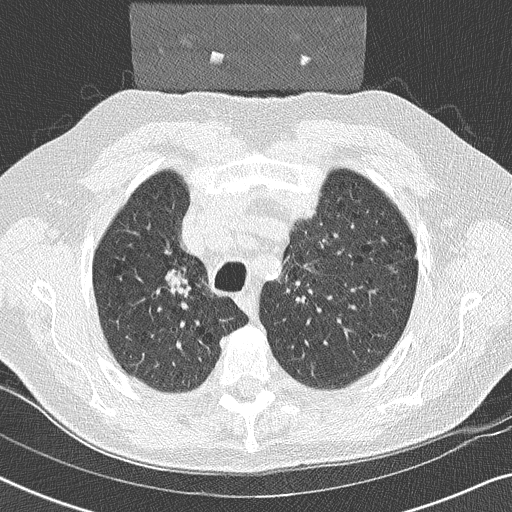
Low-dose screening chest CT, one axial slice; slice 185 of 252 in the series (ordered by position); 120 kVp; lung window (W 1500 / L -600 HU); 2 mm slice thickness; 512 × 512 image matrix, field of view 330 × 330 mm.
Structures marked on this image (expert manual segmentation):
- lesion 1 (tumor, upper lobe of right lung): bounding box (x1, y1, x2, y2) in pixels: (168, 274, 182, 288)